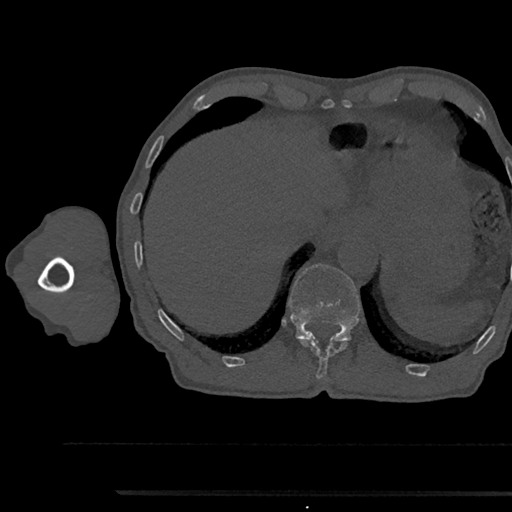
CT including the spine, one axial slice. Slice 749 of 797 in the series (ordered by position). Bone window (W 1800 / L 400 HU). 512 × 512 image matrix. Patient: male, 79 years. Case-level facts recorded for this patient, not image findings: primary cancer: prostate.
Structures marked on this image (semi-automatic segmentation, software-assisted and operator-edited):
- T11 vertebra: bounding box <301,340,346,379> (left, top, right, bottom; pixels)
- T12 vertebra: <289,264,360,342>